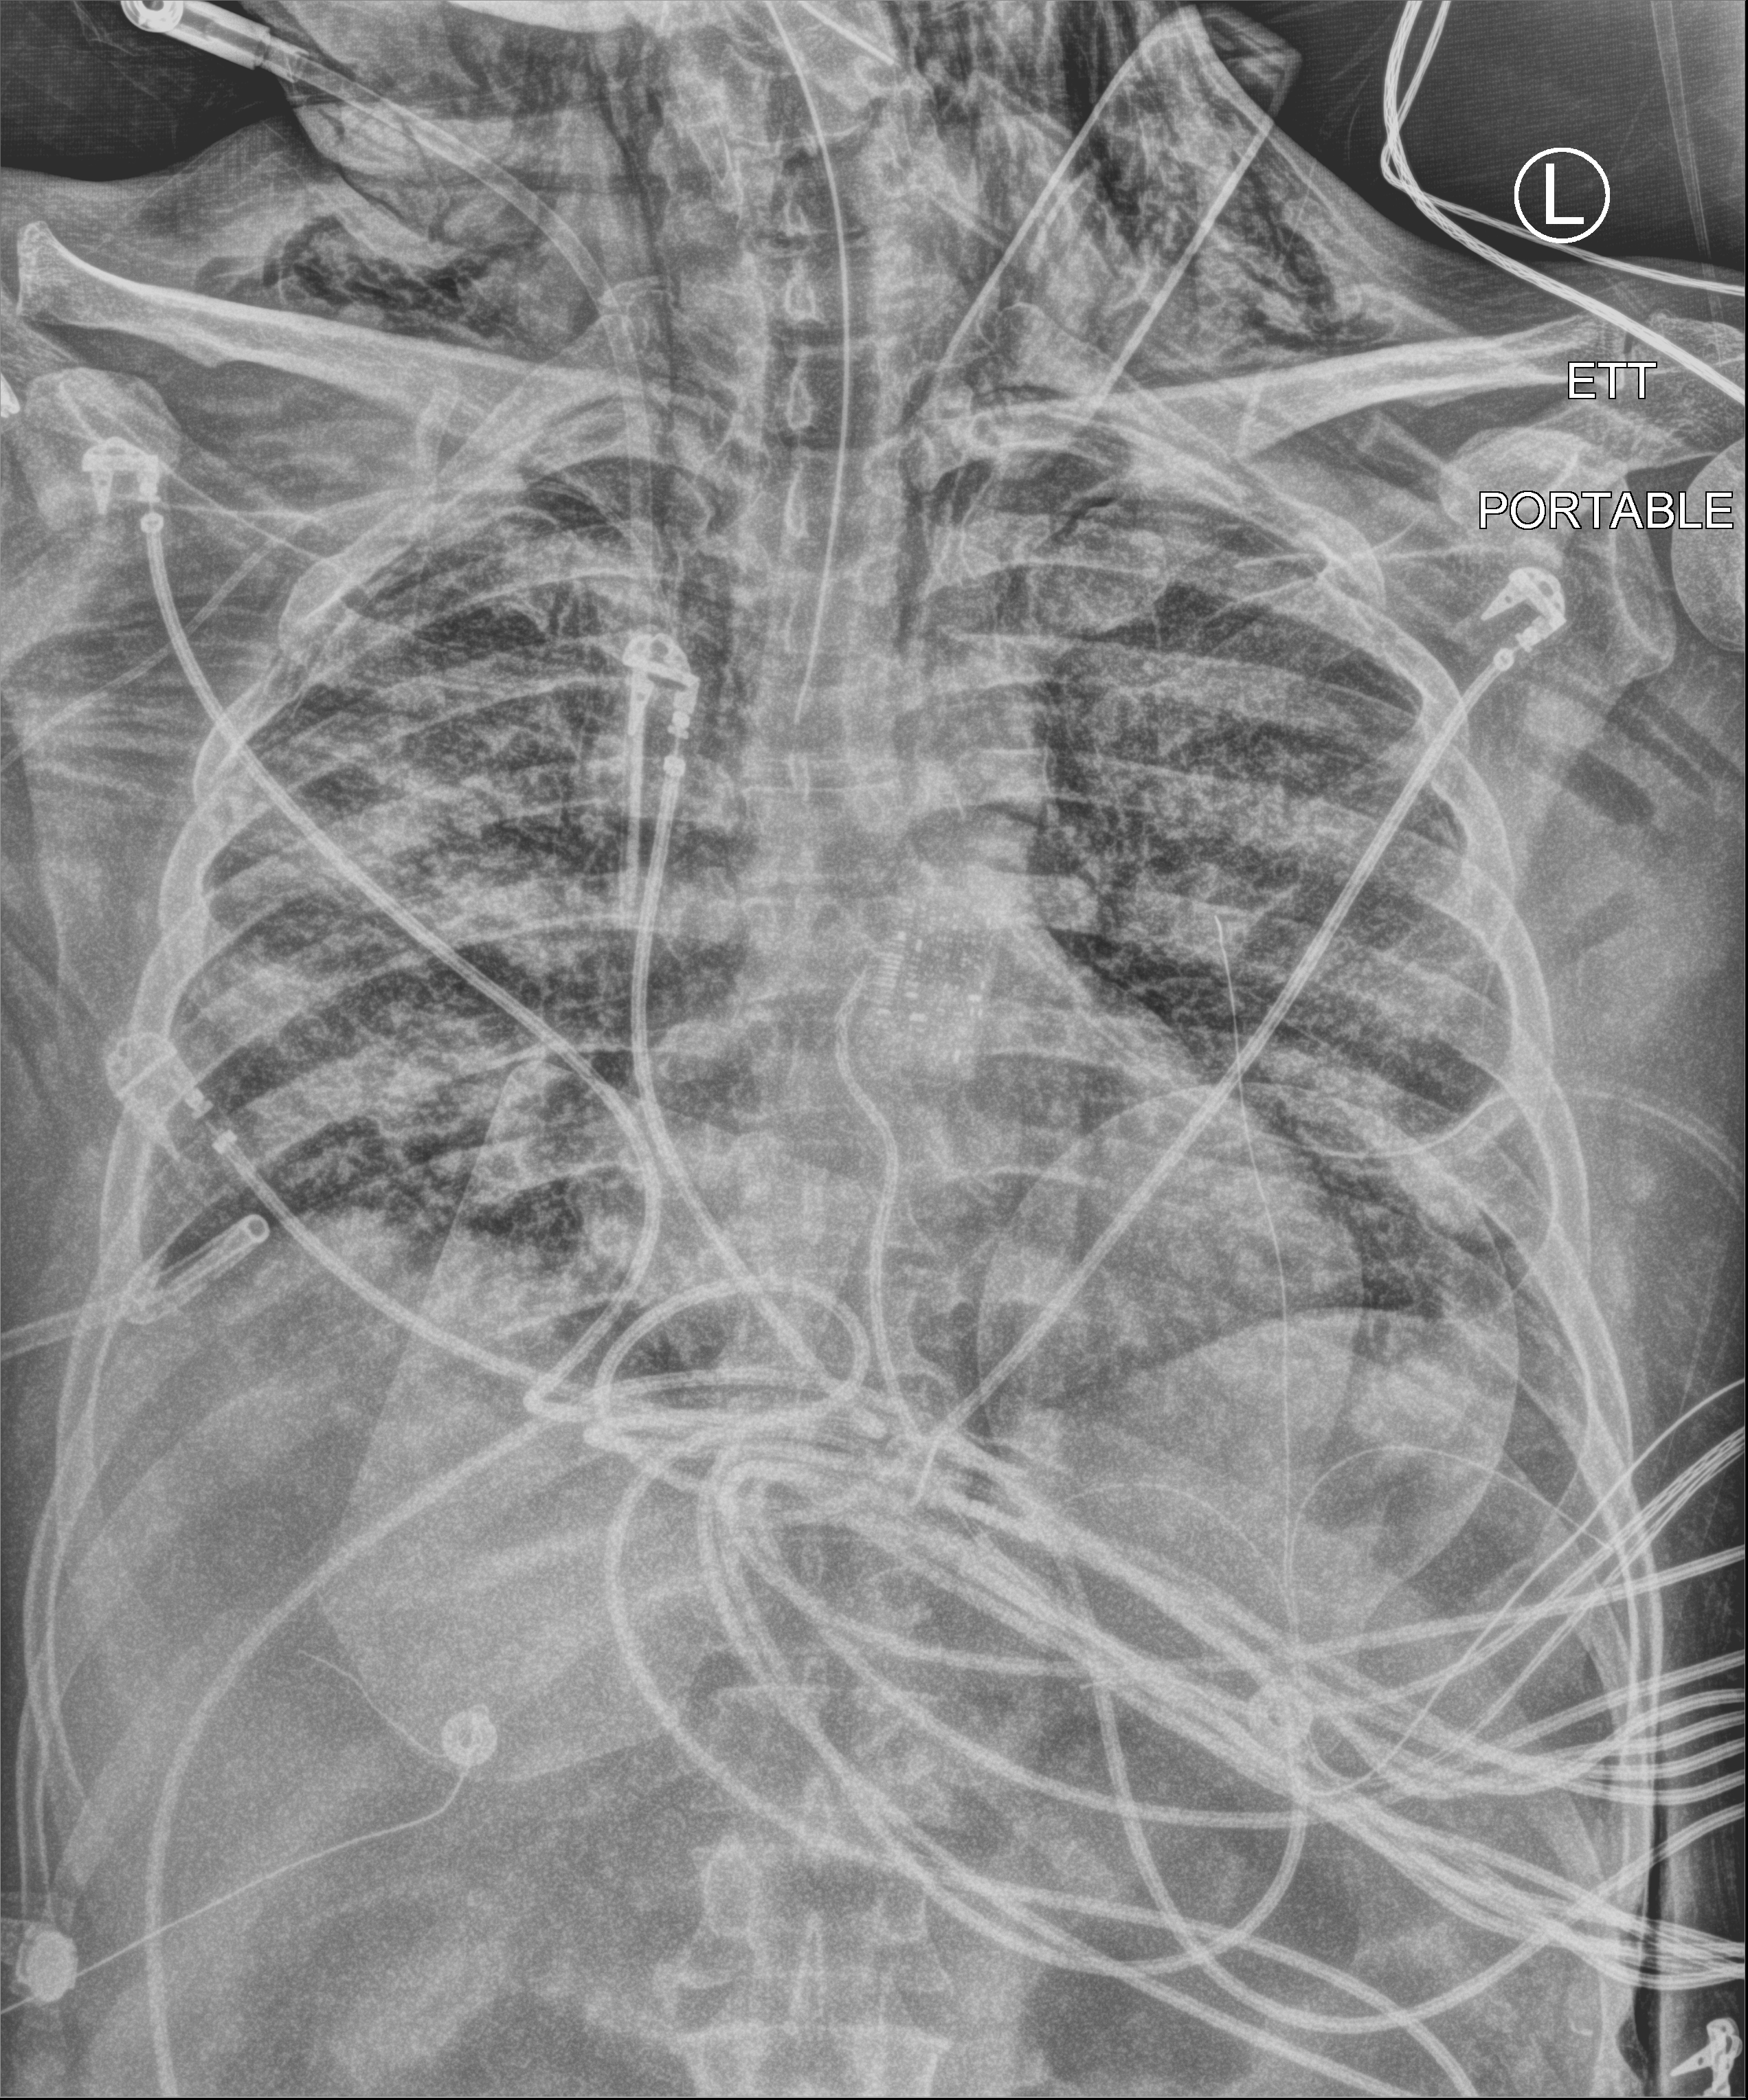
Portable chest radiograph; anteroposterior (AP) projection. Patient hospitalised with COVID-19; male, aged 18–59 years.
Hospital-stay facts (about this admission, not read from this image; timing relative to this image not recorded): length of hospital stay: 77 days; admitted to intensive care during this hospital stay: yes.